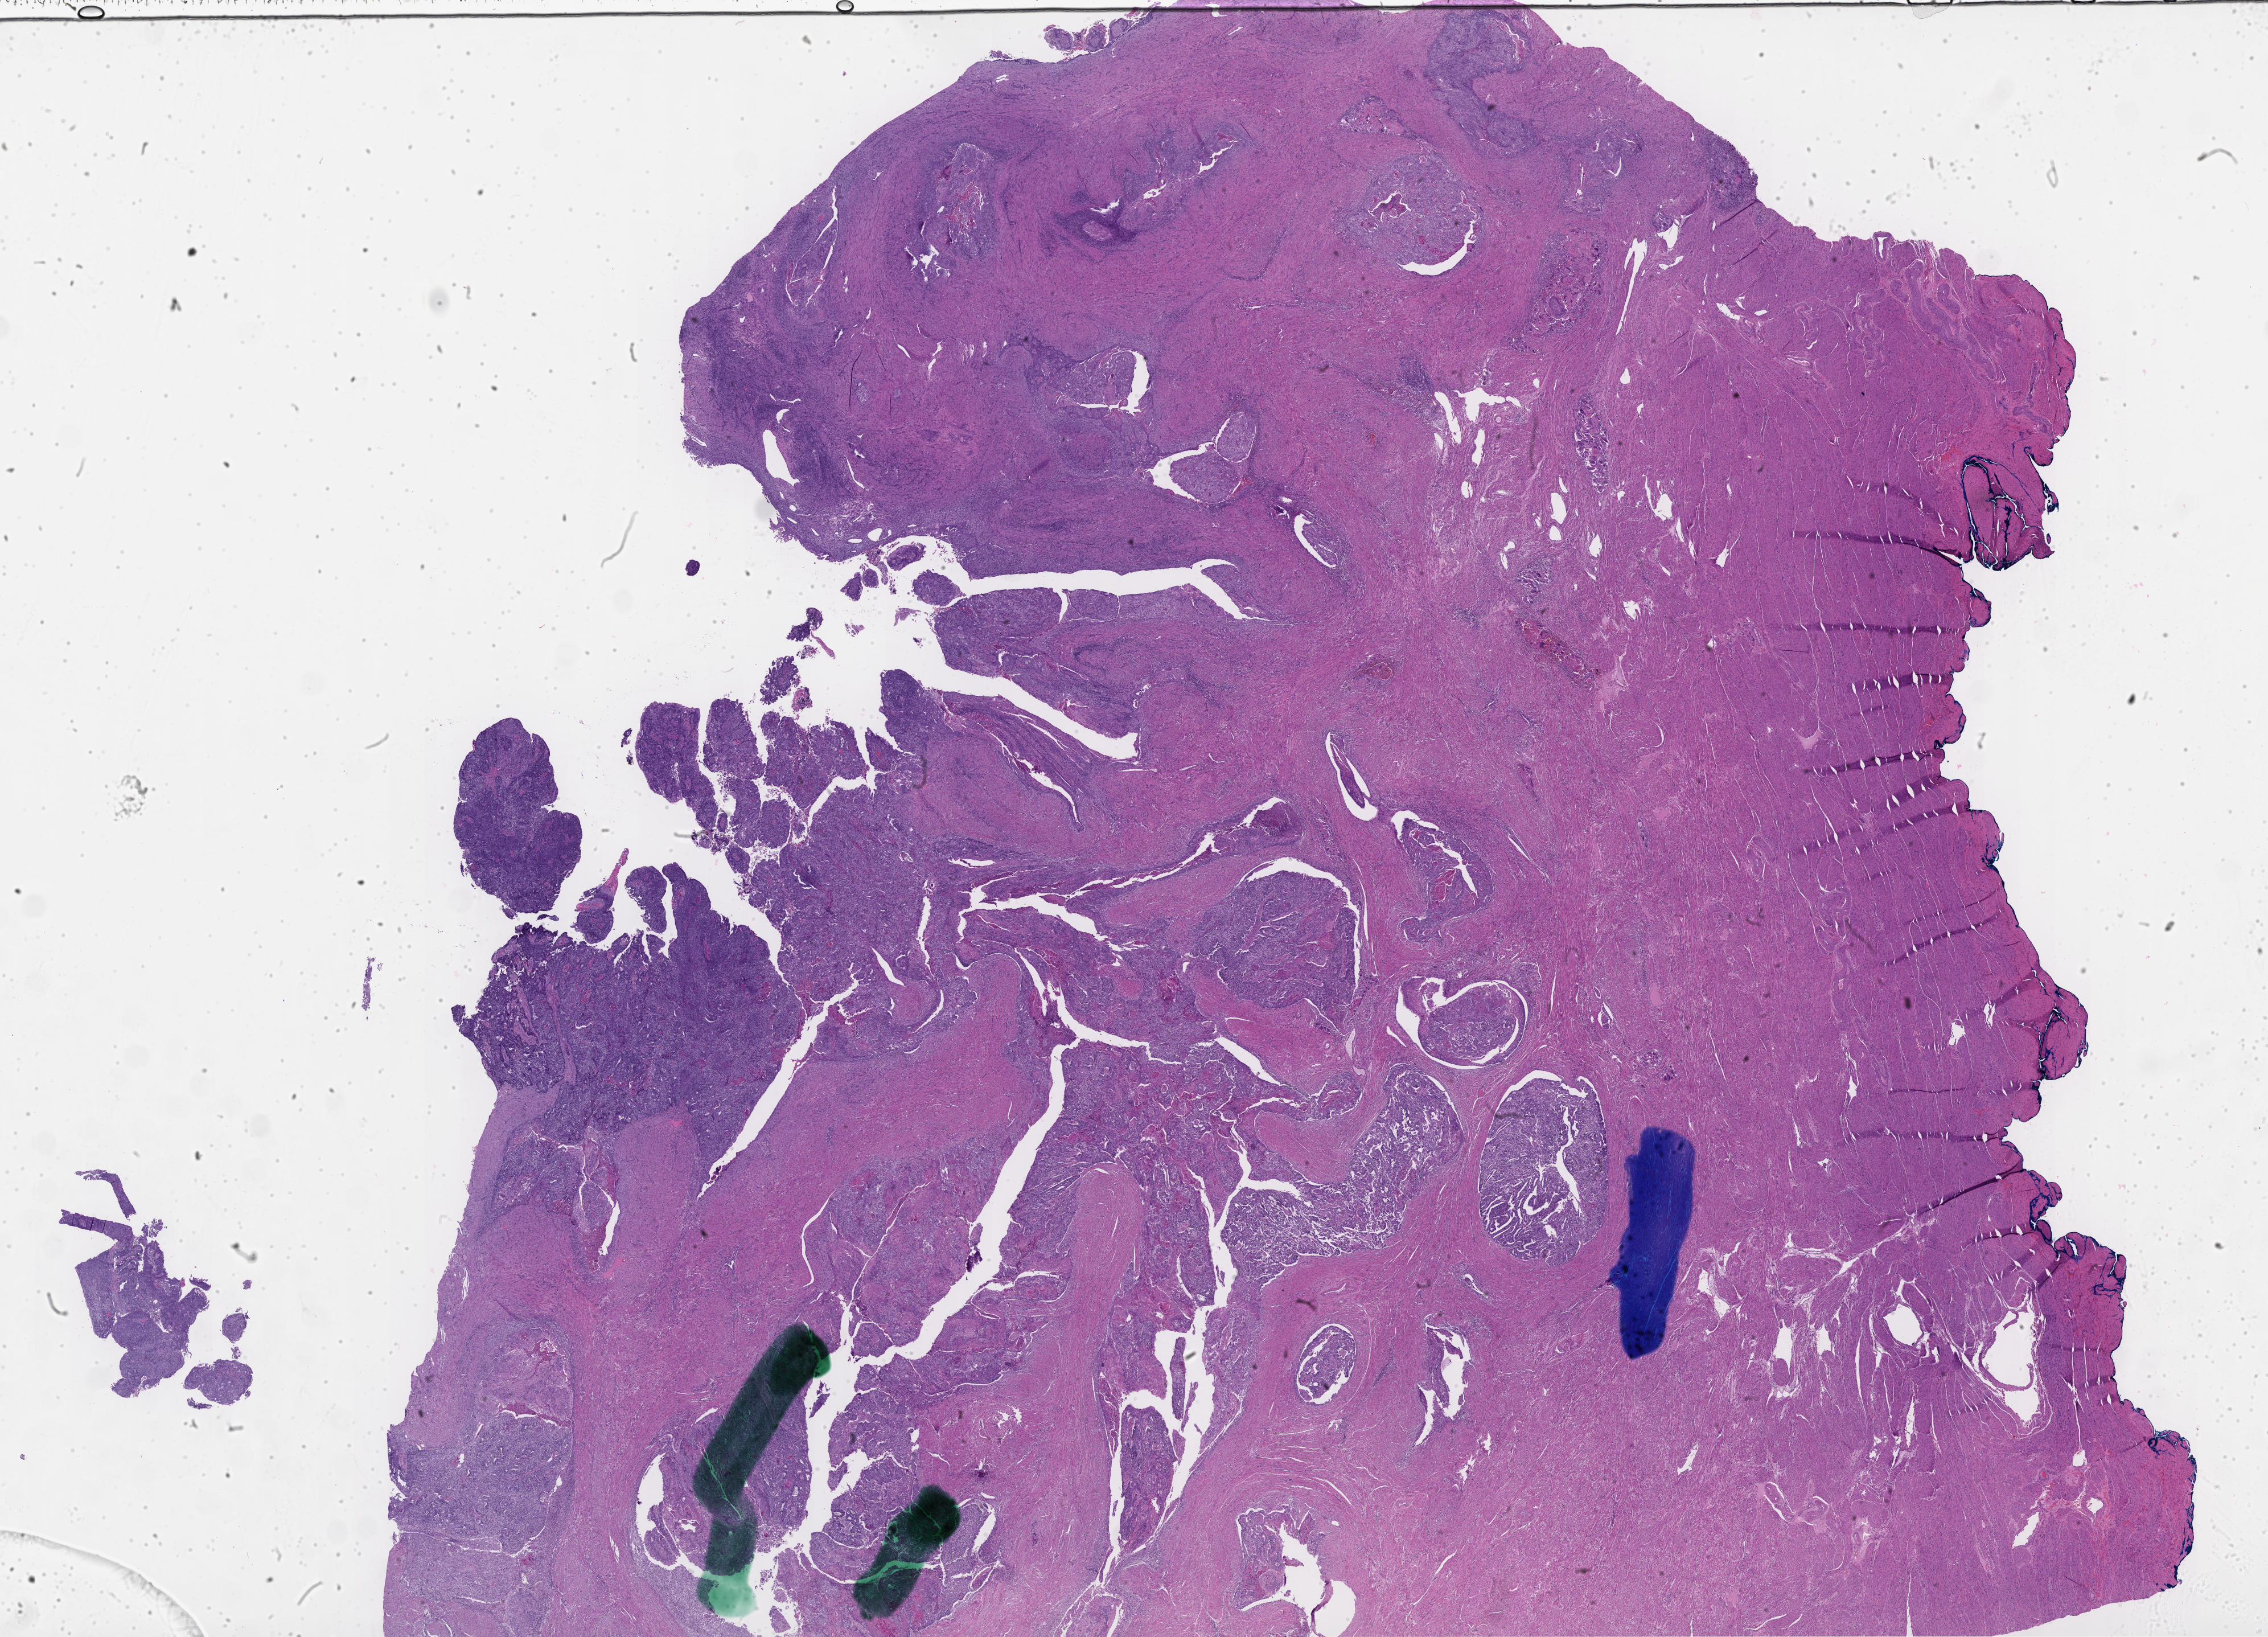
Whole-slide histology image, H&E-stained, a low-resolution overview of the entire scanned area, about 32.1 x 23.2 mm; tumour tissue sample, uterus. Female, 68 y/o.
• patient diagnosis (cohort enrolment): corpus endometrial carcinoma (uterus)